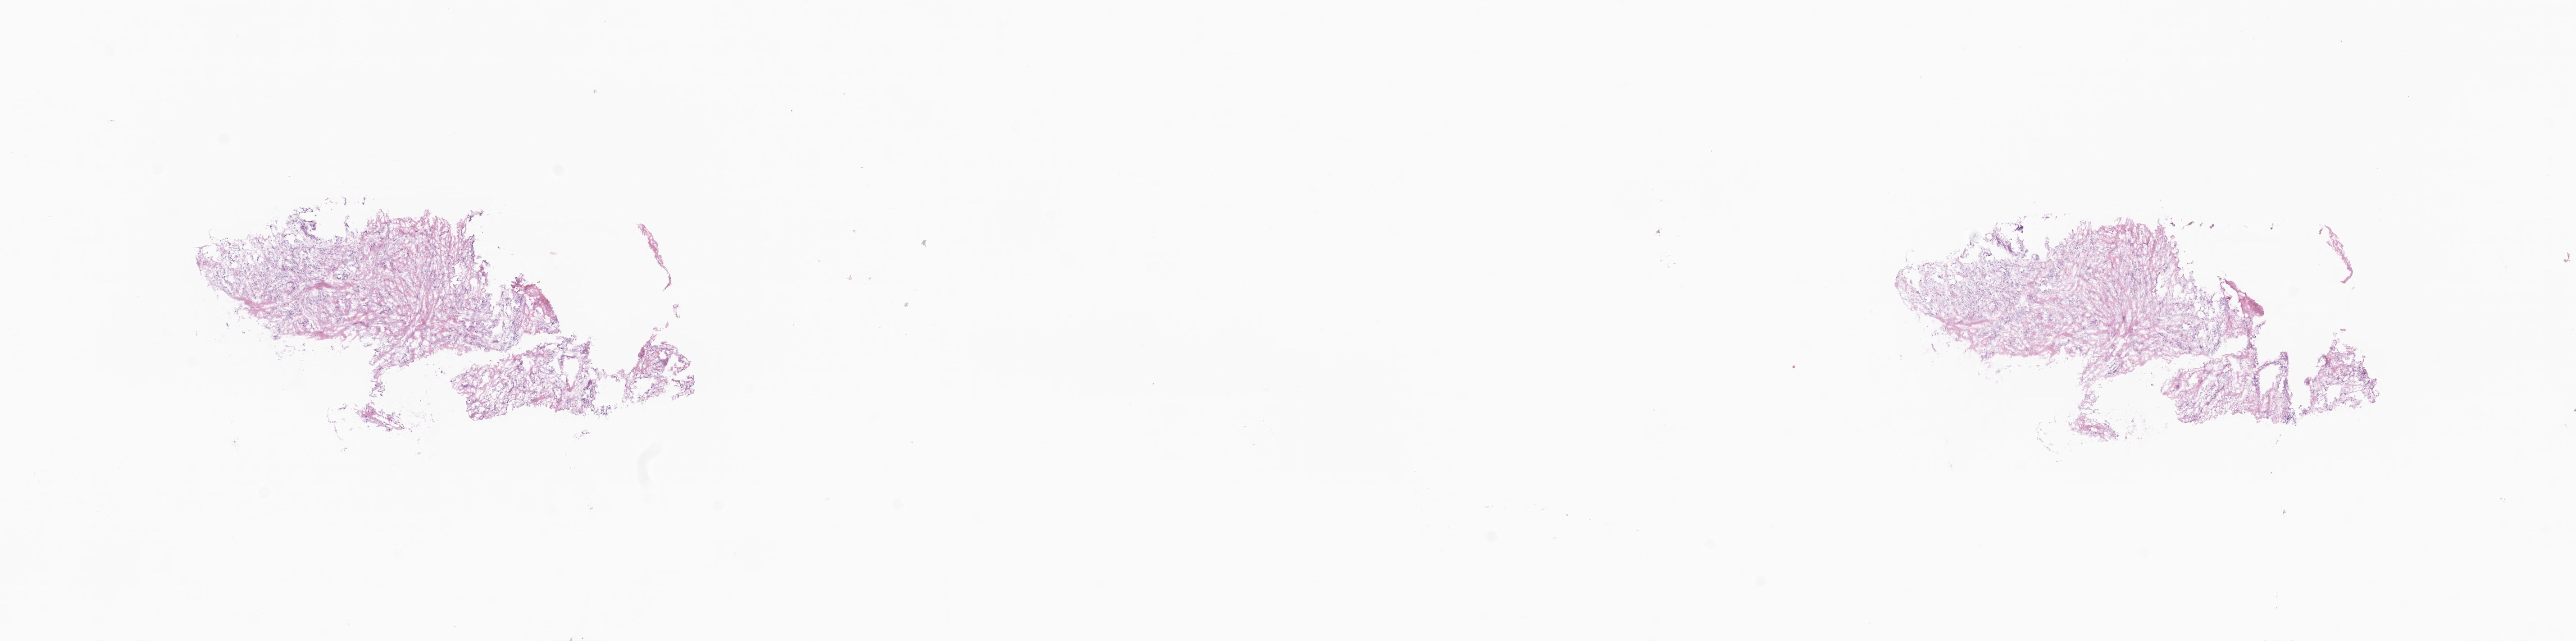
Haematoxylin and eosin whole-slide image — shown as a low-resolution overview of the whole scanned area (about 24.1 x 6.0 mm). Frozen section (tissue freezing medium). Primary tumor. Site: breast (left). Female patient; age at initial diagnosis 53 years. Pathologist review of this section (percent, as recorded): tumor cells 25%, tumor nuclei 25%, stromal cells 40%, necrosis 35%, normal cells 0%. Infiltration values recorded for this section: lymphocyte infiltration 0%, monocyte infiltration 0%, neutrophil infiltration 0%.
* section: top of the tissue portion
* histologic diagnosis: Infiltrating duct carcinoma, NOS